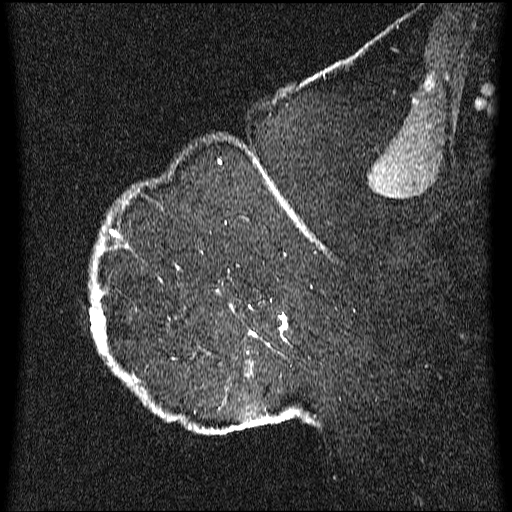
Breast MRI (dynamic contrast-enhanced), one sagittal slice. Position 48 of 64 along the scan axis. Dynamic contrast-enhanced series, image 2 of 3 at this slice position (ordered by acquisition). 1.5 T. TE 4.2 ms, TR 9.1 ms. 2.2 mm slice thickness. 512 × 512 image matrix, field of view 180 × 180 mm. Patient: female, 52 years.
Structures marked on this image (semi-automatically segmented with operator editing):
- analysis volume of interest (the breast-tissue region the enhancement analysis was run in; not a lesion): bounding box [x1, y1, x2, y2] px = [90, 203, 344, 436]
- tumour enhancement mask (voxels above the 70 % enhancement threshold inside the analysis volume of interest): [91, 203, 309, 430]